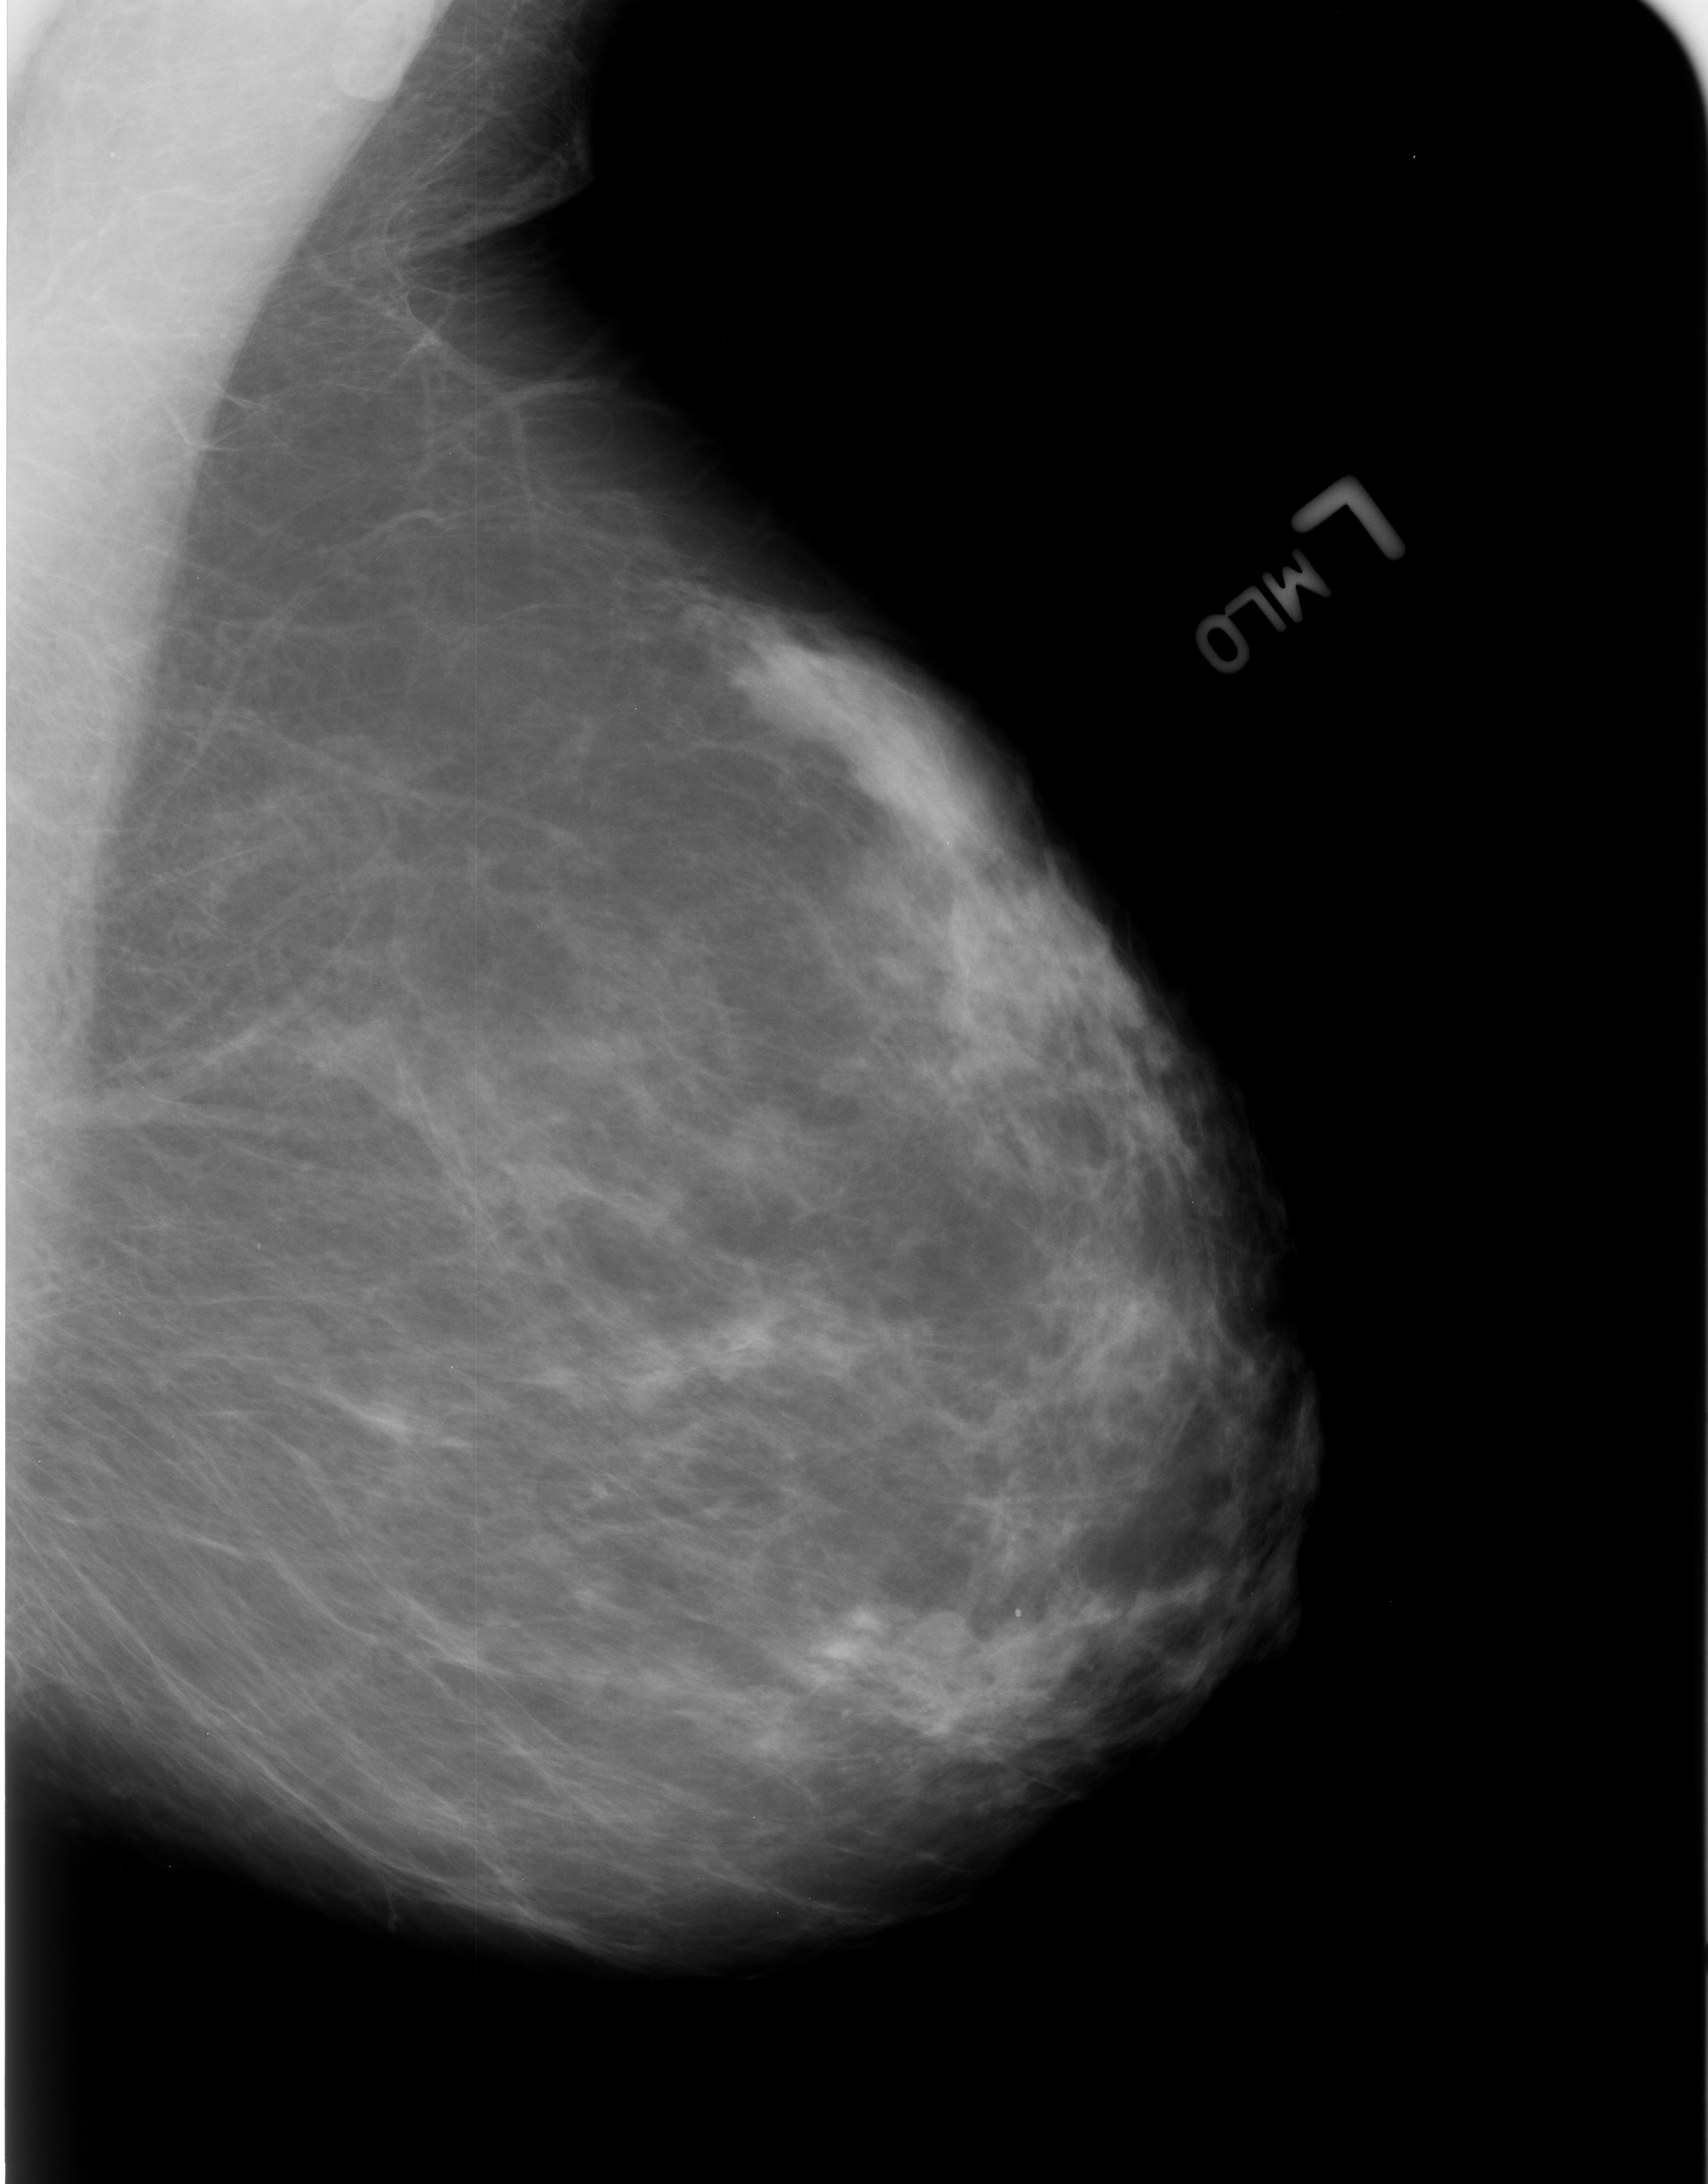
Mammogram (digitized film); left breast; mediolateral oblique (MLO) view; breast composition: scattered fibroglandular densities (BI-RADS density category 2 of 4); 1708 × 2184 image matrix.
Expert-marked regions of interest on this image (one box per marked abnormality):
- calcifications, morphology round and regular; BI-RADS assessment category 2; outcome (as recorded, no biopsy): benign without callback (not worked up further): bounding box <1001,1596,1030,1638> (left, top, right, bottom; pixels)